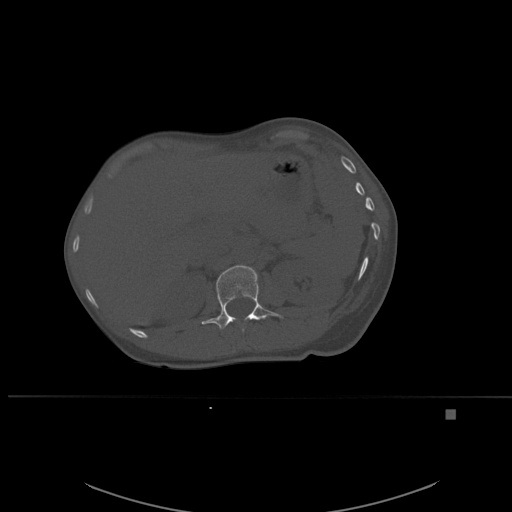
CT including the spine, one axial slice; slice 262 of 537 in the series (ordered by position); bone window (W 1800 / L 400 HU); 1.5 mm slice thickness; 512 × 512 image matrix. Female patient, age 45 years. From the clinical record (not read from this slice): primary cancer: lung.
Outlined on this slice (semi-automatic segmentation, software-assisted and operator-edited):
- L1 vertebra: bounding box <201,265,284,332> (left, top, right, bottom; pixels)